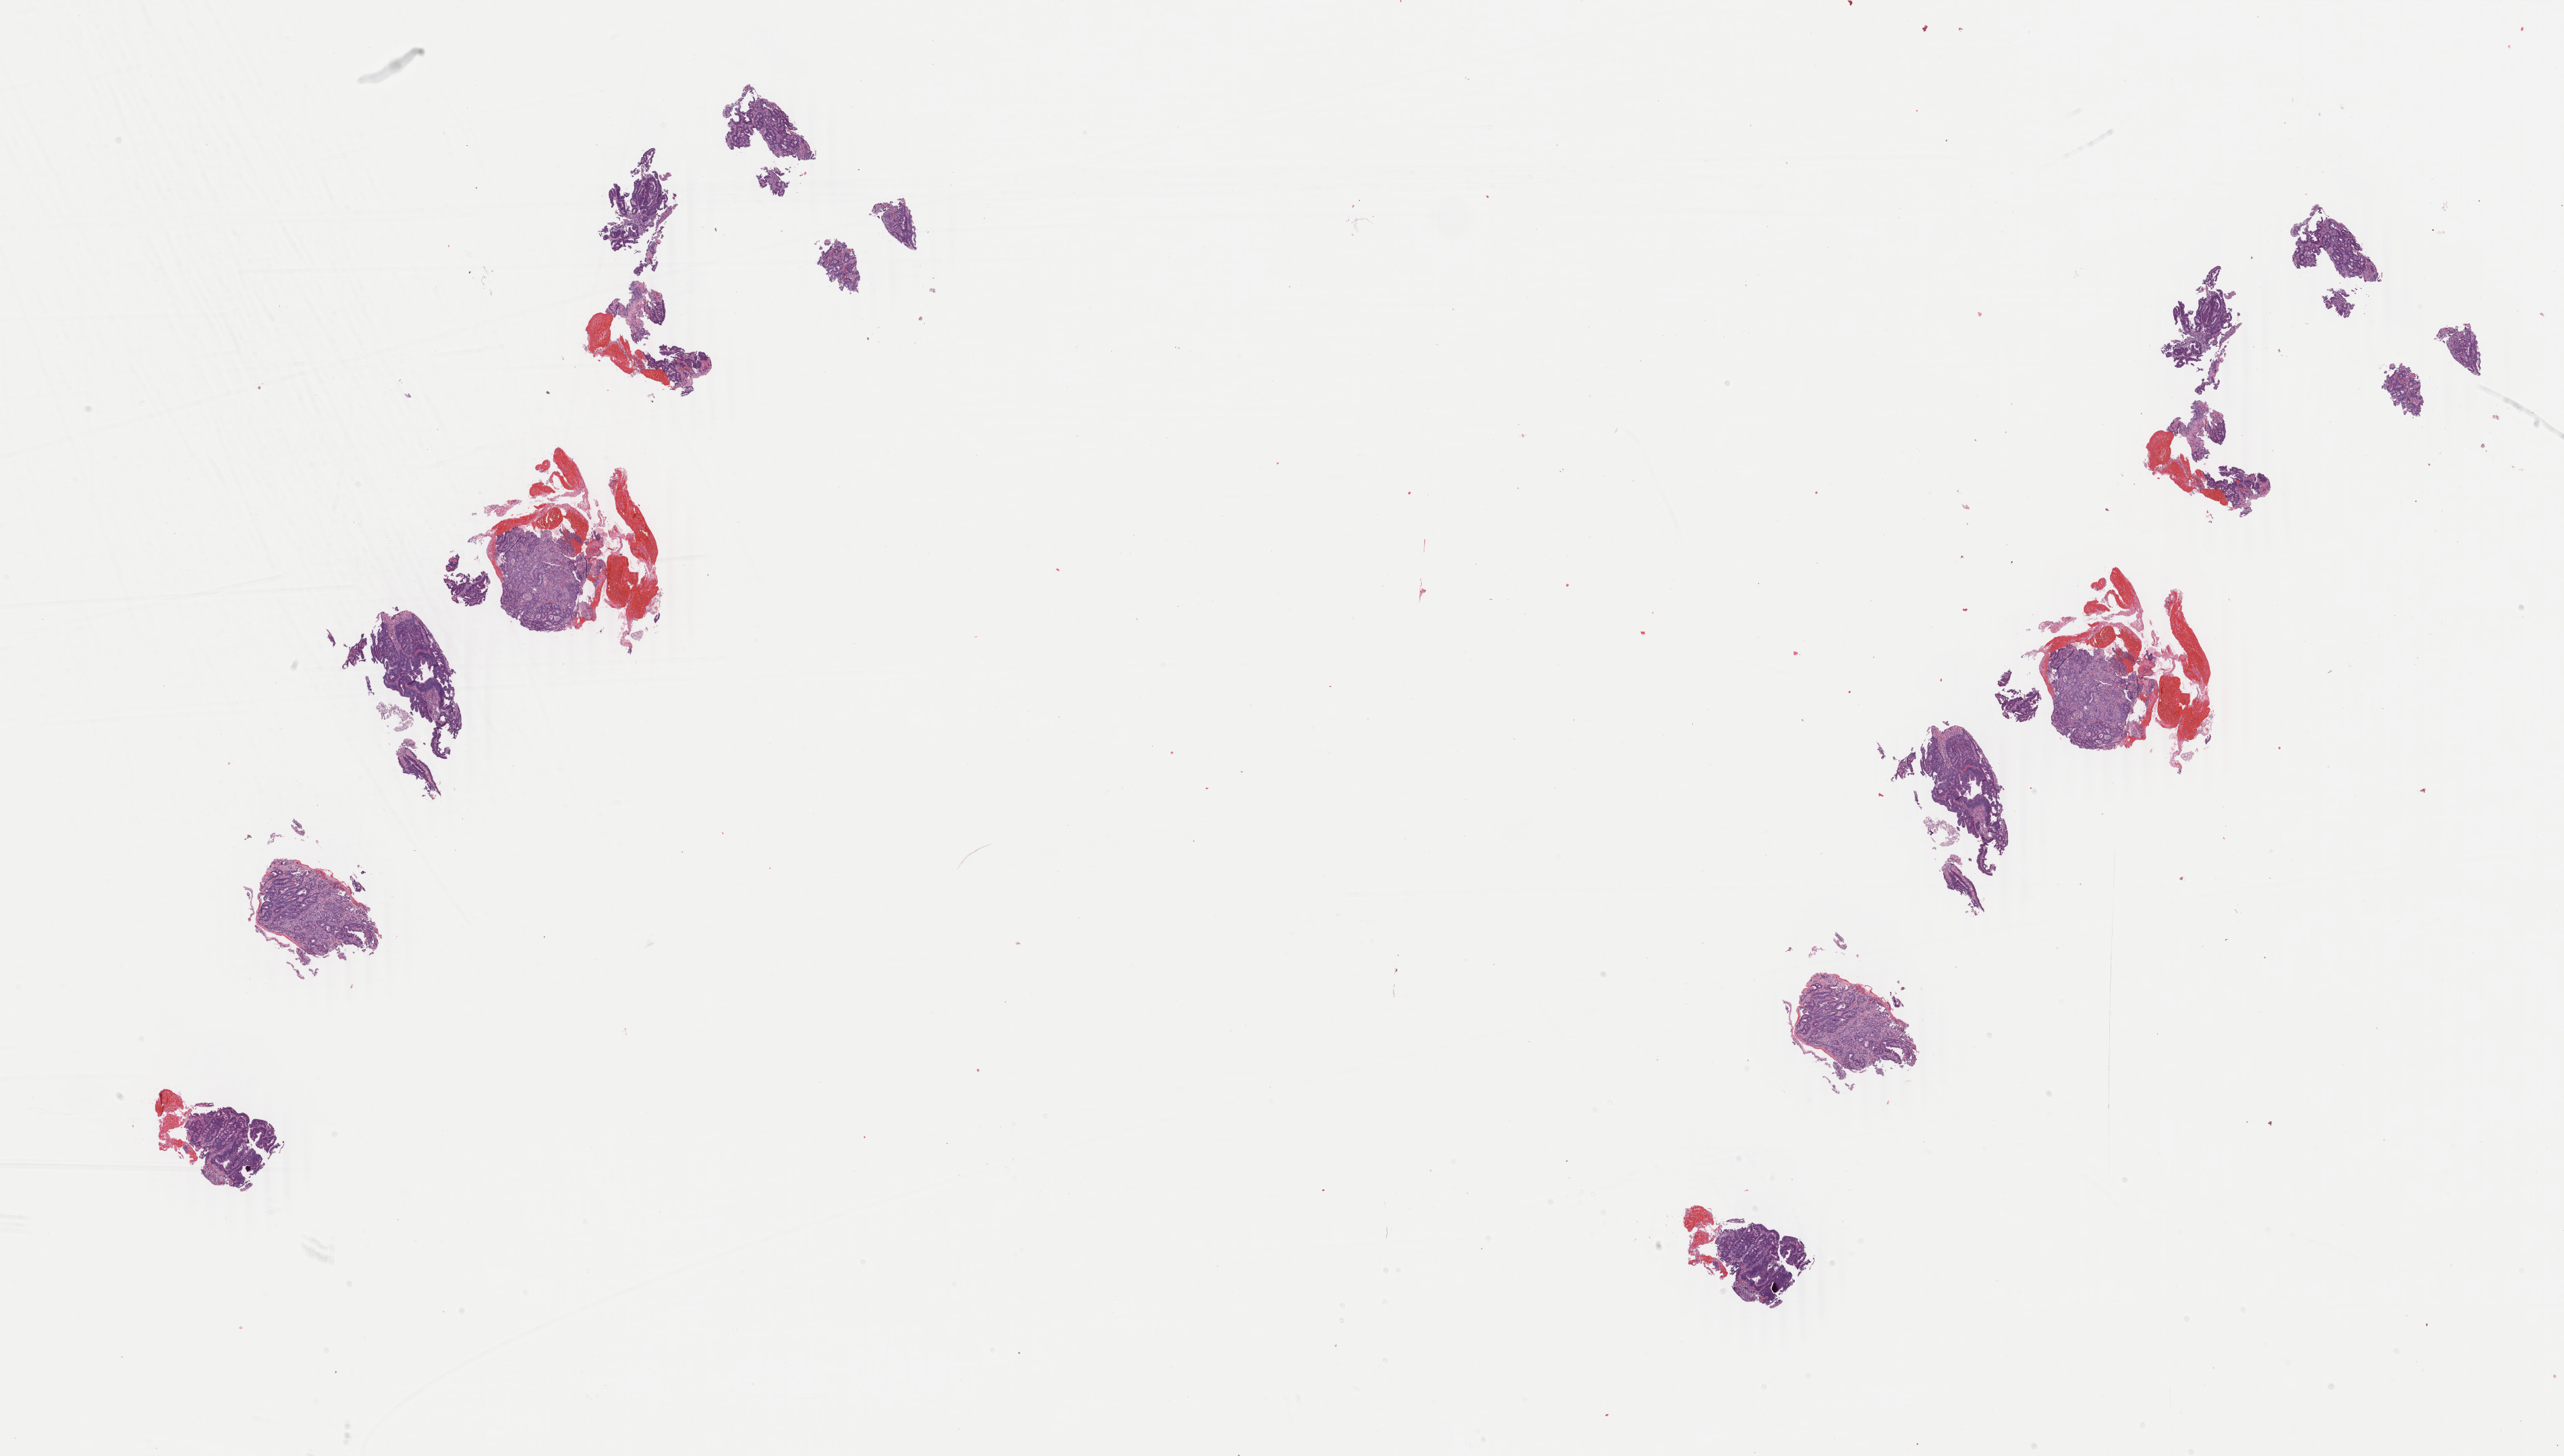
Digitized H&E-stained tissue section (whole slide) — low-resolution overview of the scanned area, about 30.2 x 17.2 mm (slide scanned at 40x), formalin-fixed paraffin-embedded (FFPE) diagnostic section, stomach, primary tumour sample. Female patient; age at initial diagnosis 65 years. Histologic grade: G2 (moderately differentiated). Composition of this section per pathologist review: tumour cells 70%, tumour nuclei 80%, normal cells 1%, stromal cells 25%, necrosis 4%. Infiltration values recorded for this section: lymphocyte infiltration 5%, monocyte infiltration 2%, neutrophil infiltration 10%.
- TNM: T4a N1 M1
- AJCC pathologic stage: IV
- pathologic diagnosis: Adenocarcinoma, intestinal type